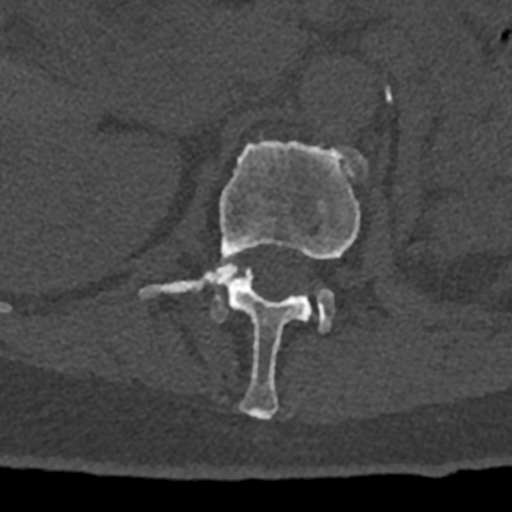
CT including the spine, one axial slice; slice 424 of 797 in the series (ordered by position); reconstruction kernel Br40s/3; 120 kVp; bone window (W 1800 / L 400 HU); 512 × 512 image matrix, field of view 160 × 160 mm. Patient: male, 74 years. From the clinical record (not read from this slice): primary cancer: renal; vertebrae with lytic lesions (as recorded): T10, L1, L2, L3, L4, L5.
Structures marked on this image (semi-automatic segmentation, software-assisted and operator-edited):
- L1 vertebra: bounding box [x1, y1, x2, y2] px = [139, 140, 367, 420]
- L2 vertebra: [211, 268, 334, 332]